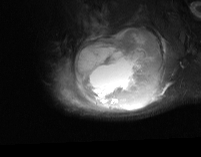
MRI of an extremity soft-tissue mass, one axial slice. Position 51 of 74 along the scan axis. STIR. MR volume resampled by the dataset authors to the PET/CT grid (not the native acquisition matrix). 3.27 mm slice thickness. 201 × 157 image matrix. Male patient. From the clinical record (not read from this slice): histological type: pleiomorphic spindle cell undifferentiated; grade: high; site of the primary tumour: right parascapusular.
Structures marked on this image (expert contour drawn on MRI and transferred to this co-registered scan by the dataset authors):
- gross tumour volume including surrounding oedema: bounding box <53,27,177,115> (left, top, right, bottom; pixels)
- gross tumour volume (mass): <74,30,161,110>